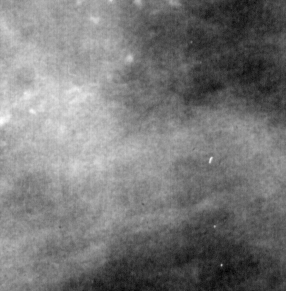
Region of interest cut from a scanned film mammogram (one marked finding), left breast, MLO view.
Calcifications, morphology pleomorphic, distribution clustered; BI-RADS assessment category 4; pathology (as recorded): malignant.